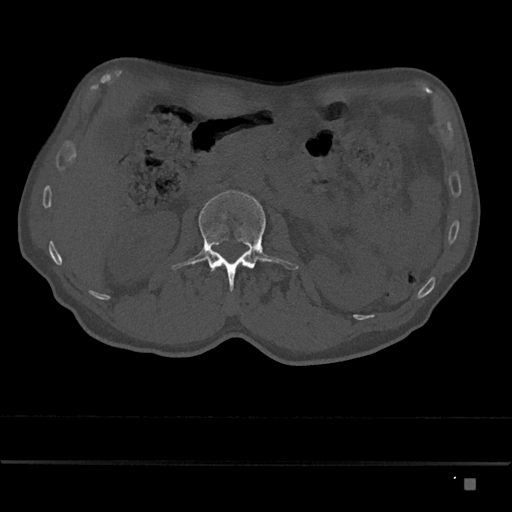
CT including the spine, one axial slice; slice 479 of 797 in the series (ordered by position); reconstruction kernel Br40s/3; bone window (W 1800 / L 400 HU); 512 × 512 image matrix, field of view 390 × 390 mm. Male patient, age 72 years. From the clinical record (not read from this slice): primary cancer: prostate.
Structures marked on this image (semi-automatic segmentation, software-assisted and operator-edited):
- L2 vertebra: bounding box (x1, y1, x2, y2) in pixels: (171, 190, 299, 292)